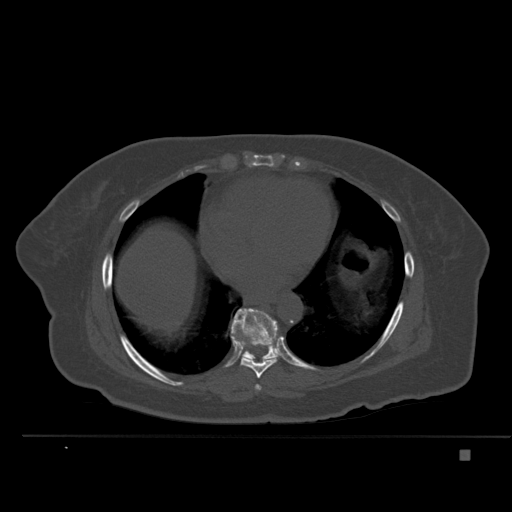
CT including the spine, one axial slice. Slice 307 of 477 in the series (ordered by position). Bone window (W 1800 / L 400 HU). 1.5 mm slice thickness. 512 × 512 image matrix, field of view 422 × 422 mm. Female patient, age 74 years. Case-level facts recorded for this patient, not image findings: primary cancer: colon.
Outlined on this slice (semi-automatically segmented with operator editing):
- T7 vertebra: bounding box [x1, y1, x2, y2] px = [255, 339, 271, 391]
- T8 vertebra: [232, 333, 278, 378]
- T9 vertebra: [231, 308, 279, 362]